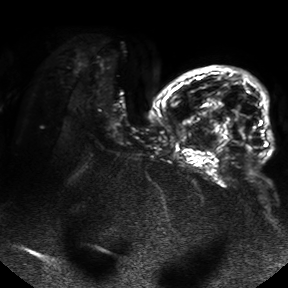
Breast MRI, one axial slice; position 24 of 50 along the scan axis; diffusion-weighted series; image 2 of 4 stored at this slice position (different b-values; order by instance number); 1.5 T; 288 × 288 image matrix. Female patient.
Structures marked on this image (outlined manually by an expert reader):
- tumour on diffusion-weighted imaging: bounding box <233,109,246,146> (left, top, right, bottom; pixels)